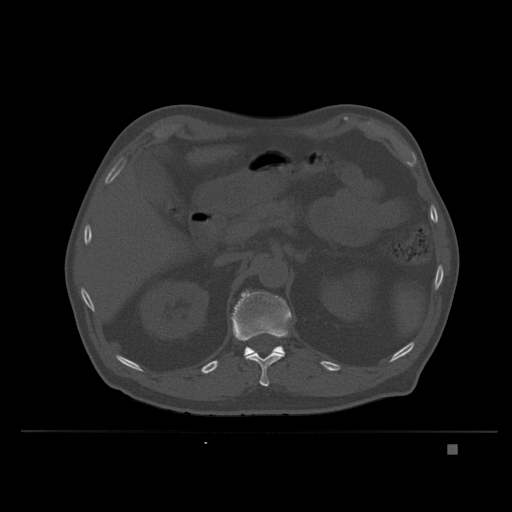
CT including the spine, one axial slice; position 149 of 435 along the scan axis; bone window (W 1800 / L 400 HU); 1.5 mm slice thickness; 512 × 512 image matrix. Patient: male, 73 years. From the clinical record (not read from this slice): primary cancer: skin.
Annotated regions visible in this slice (semi-automatic segmentation, software-assisted and operator-edited):
- L1 vertebra: bounding box (x1, y1, x2, y2) in pixels: (230, 290, 292, 359)
- T12 vertebra: (246, 352, 284, 387)